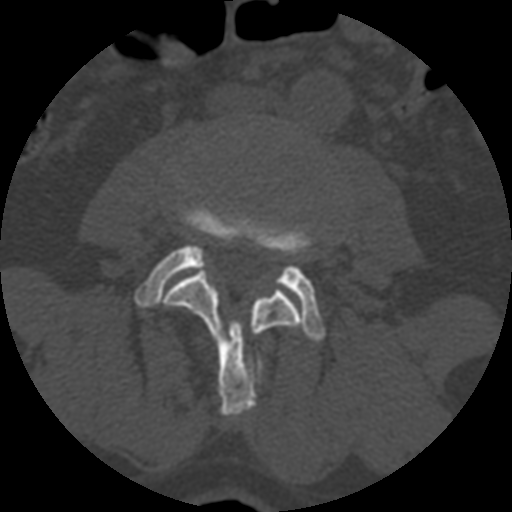
CT including the spine, one axial slice; position 294 of 399 along the scan axis; reconstruction kernel STANDARD; bone window (W 1800 / L 400 HU); 1.25 mm slice thickness; 512 × 512 image matrix, field of view 160 × 160 mm. Patient age 71 years. Case-level facts recorded for this patient, not image findings: primary cancer: prostate.
Structures marked on this image (semi-automatically segmented with operator editing):
- L3 vertebra: box from (x=163, y=268) to (x=302, y=416) px
- L4 vertebra: (x=135, y=203)–(x=325, y=342)